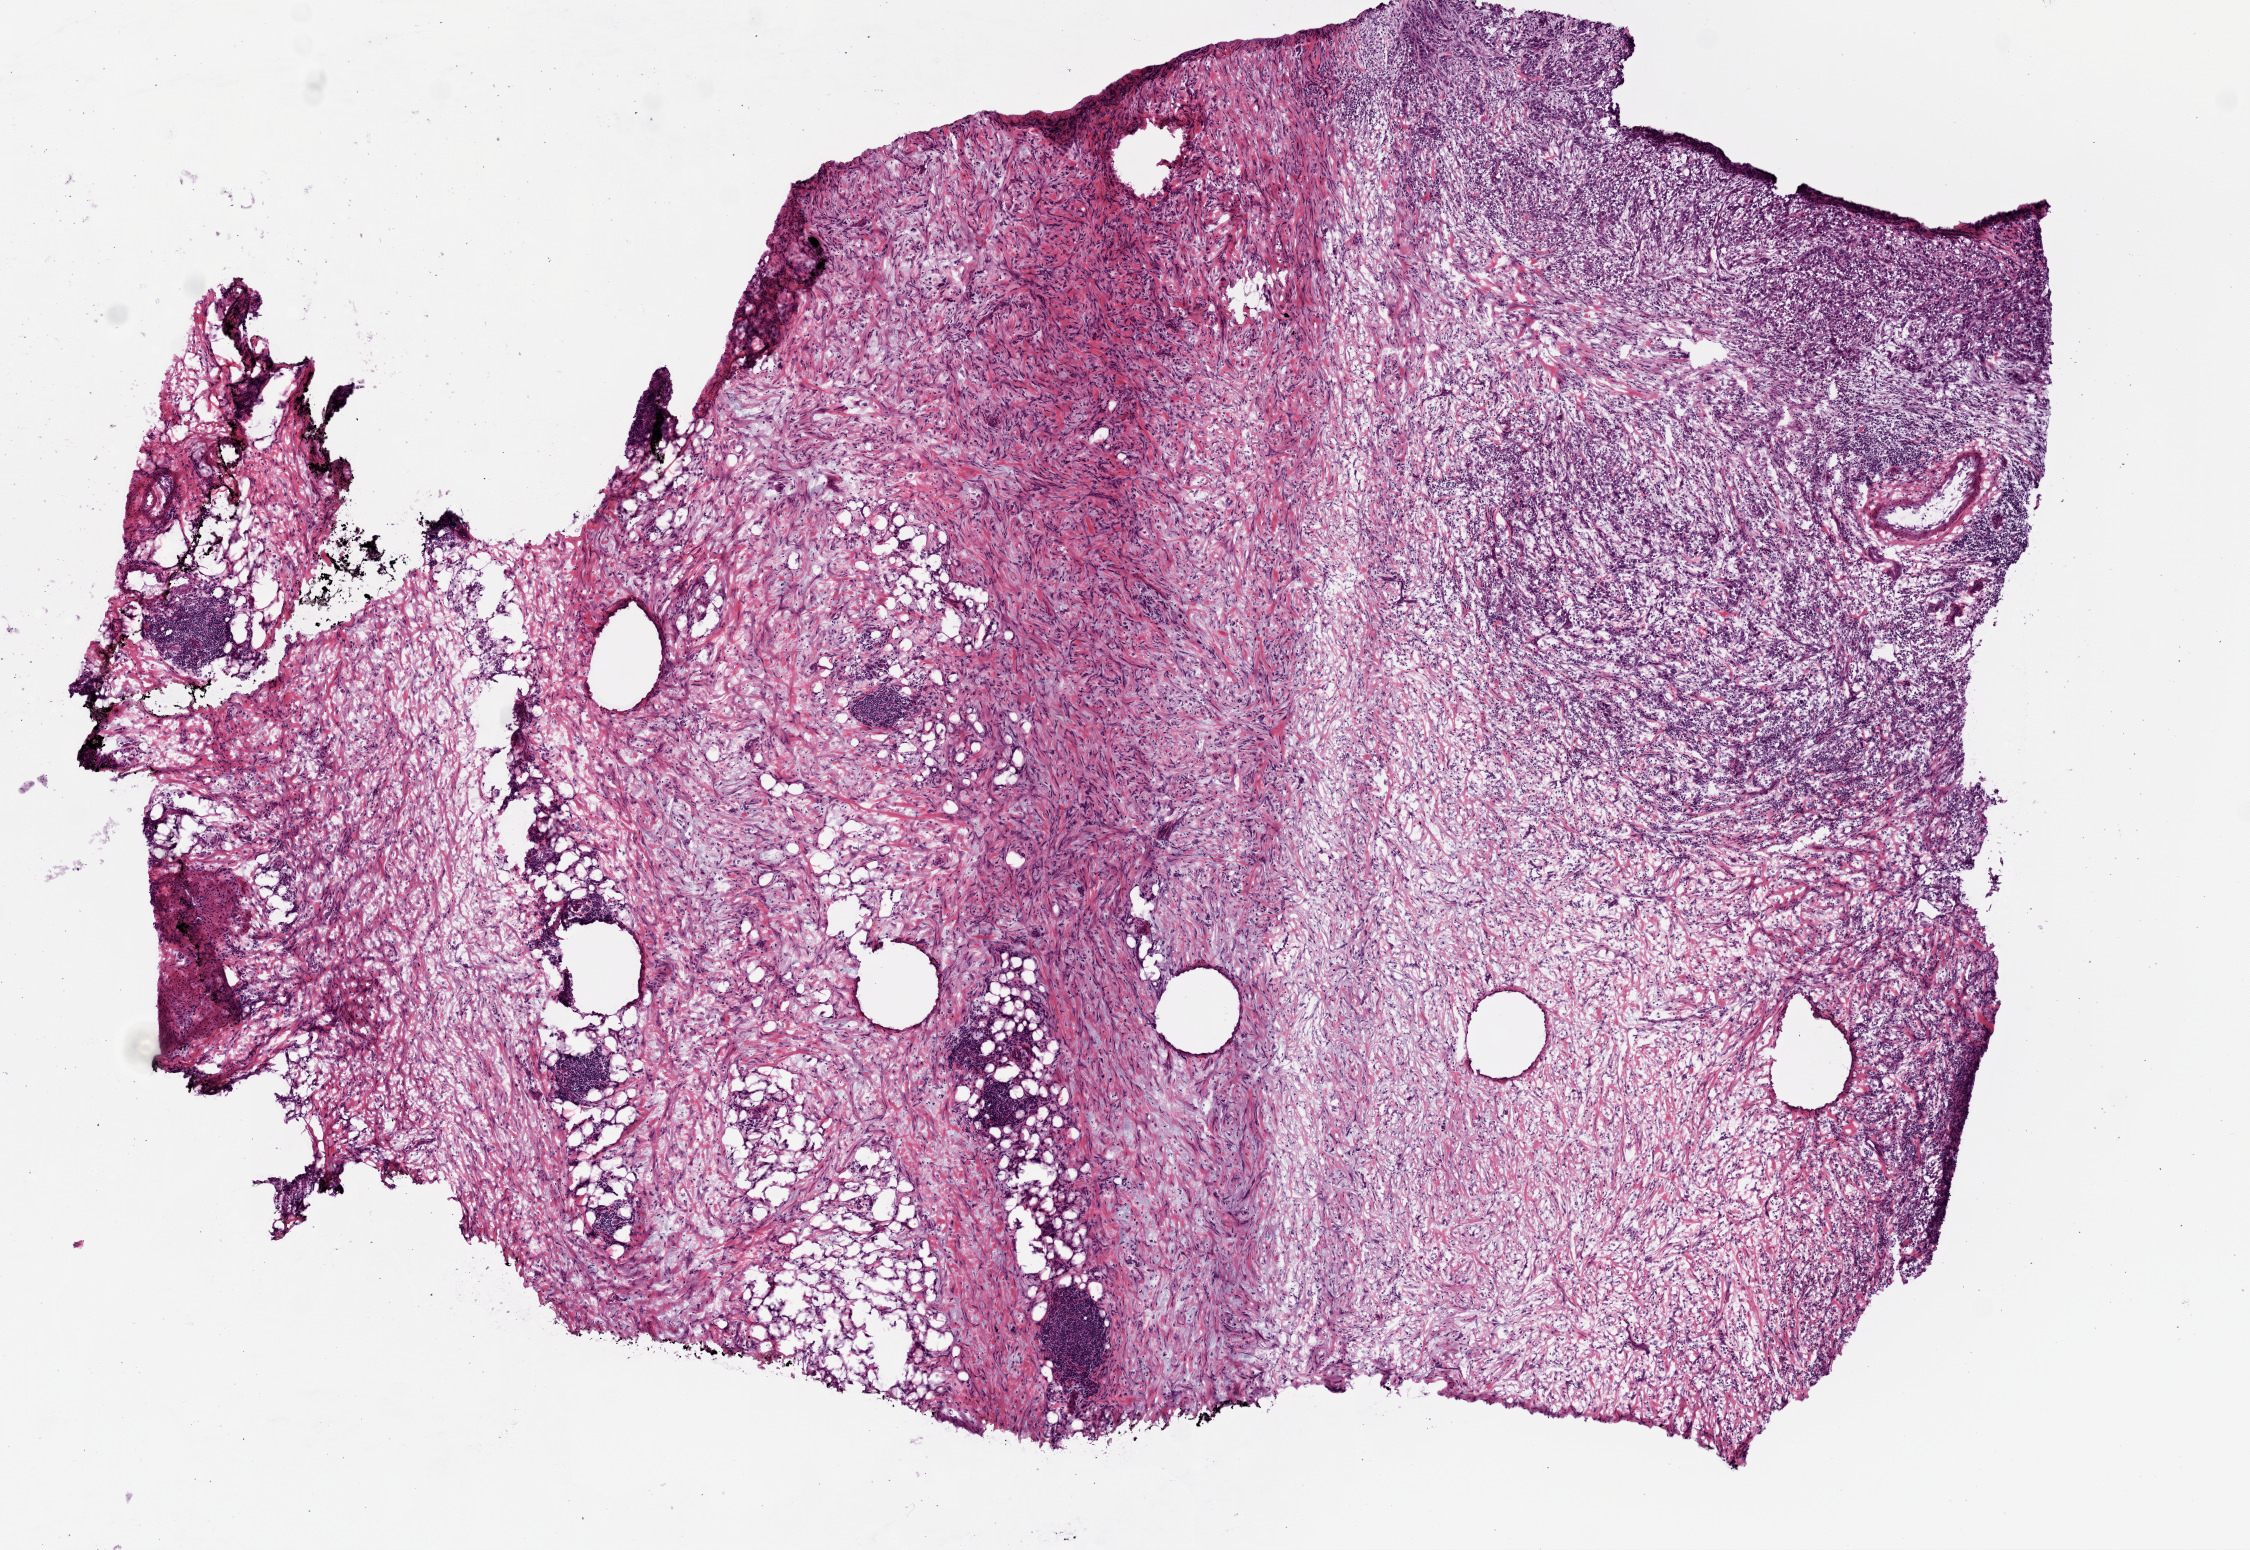
Hematoxylin and eosin (H&E) stained whole-slide image — shown as a low-resolution overview of the whole scanned area (about 9.0 x 6.2 mm); frozen section from the top of the tissue portion; sample: primary tumour, bladder. Patient: male, age at initial diagnosis 59 years. Histologic grade: high grade. Slide review estimates, as recorded: tumour cells 85%, tumour nuclei 60%, normal cells 0%, stromal cells 15%, necrosis 0%. Inflammatory infiltration, as recorded: lymphocyte infiltration 0%, monocyte infiltration 0%, neutrophil infiltration 0%.
* TNM: T2b N0 M0
* AJCC pathologic stage: II (7th edition)
* diagnosis: Transitional cell carcinoma